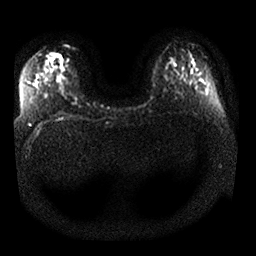
Breast MRI, one axial slice; position 13 of 25 along the scan axis; diffusion-weighted series; image 2 of 4 stored at this slice position (different b-values; order by instance number); 1.5 T; 4 mm slice thickness; 256 × 256 image matrix. Female patient.
Outlined on this slice (outlined manually by an expert reader):
- tumour on diffusion-weighted imaging: box from (x=45, y=53) to (x=62, y=64) px